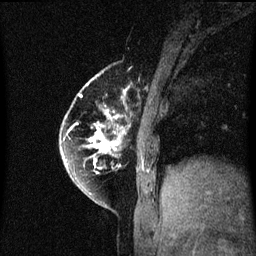
Breast MRI (dynamic contrast-enhanced), one sagittal slice. Slice 15 of 60 in the series (ordered by position). Dynamic contrast-enhanced series, image 2 of 3 at this slice position (ordered by acquisition). 1.5 T. TE 4.2 ms, TR 8.4 ms. 2 mm slice thickness. 256 × 256 image matrix, field of view 200 × 200 mm. Patient: female, 60 years.
Annotated regions visible in this slice (semi-automatically segmented with operator editing):
- analysis volume of interest (the breast-tissue region the enhancement analysis was run in; not a lesion): box from (x=64, y=70) to (x=129, y=195) px
- tumour enhancement mask (voxels above the 70 % enhancement threshold inside the analysis volume of interest): (x=64, y=76)–(x=129, y=195)